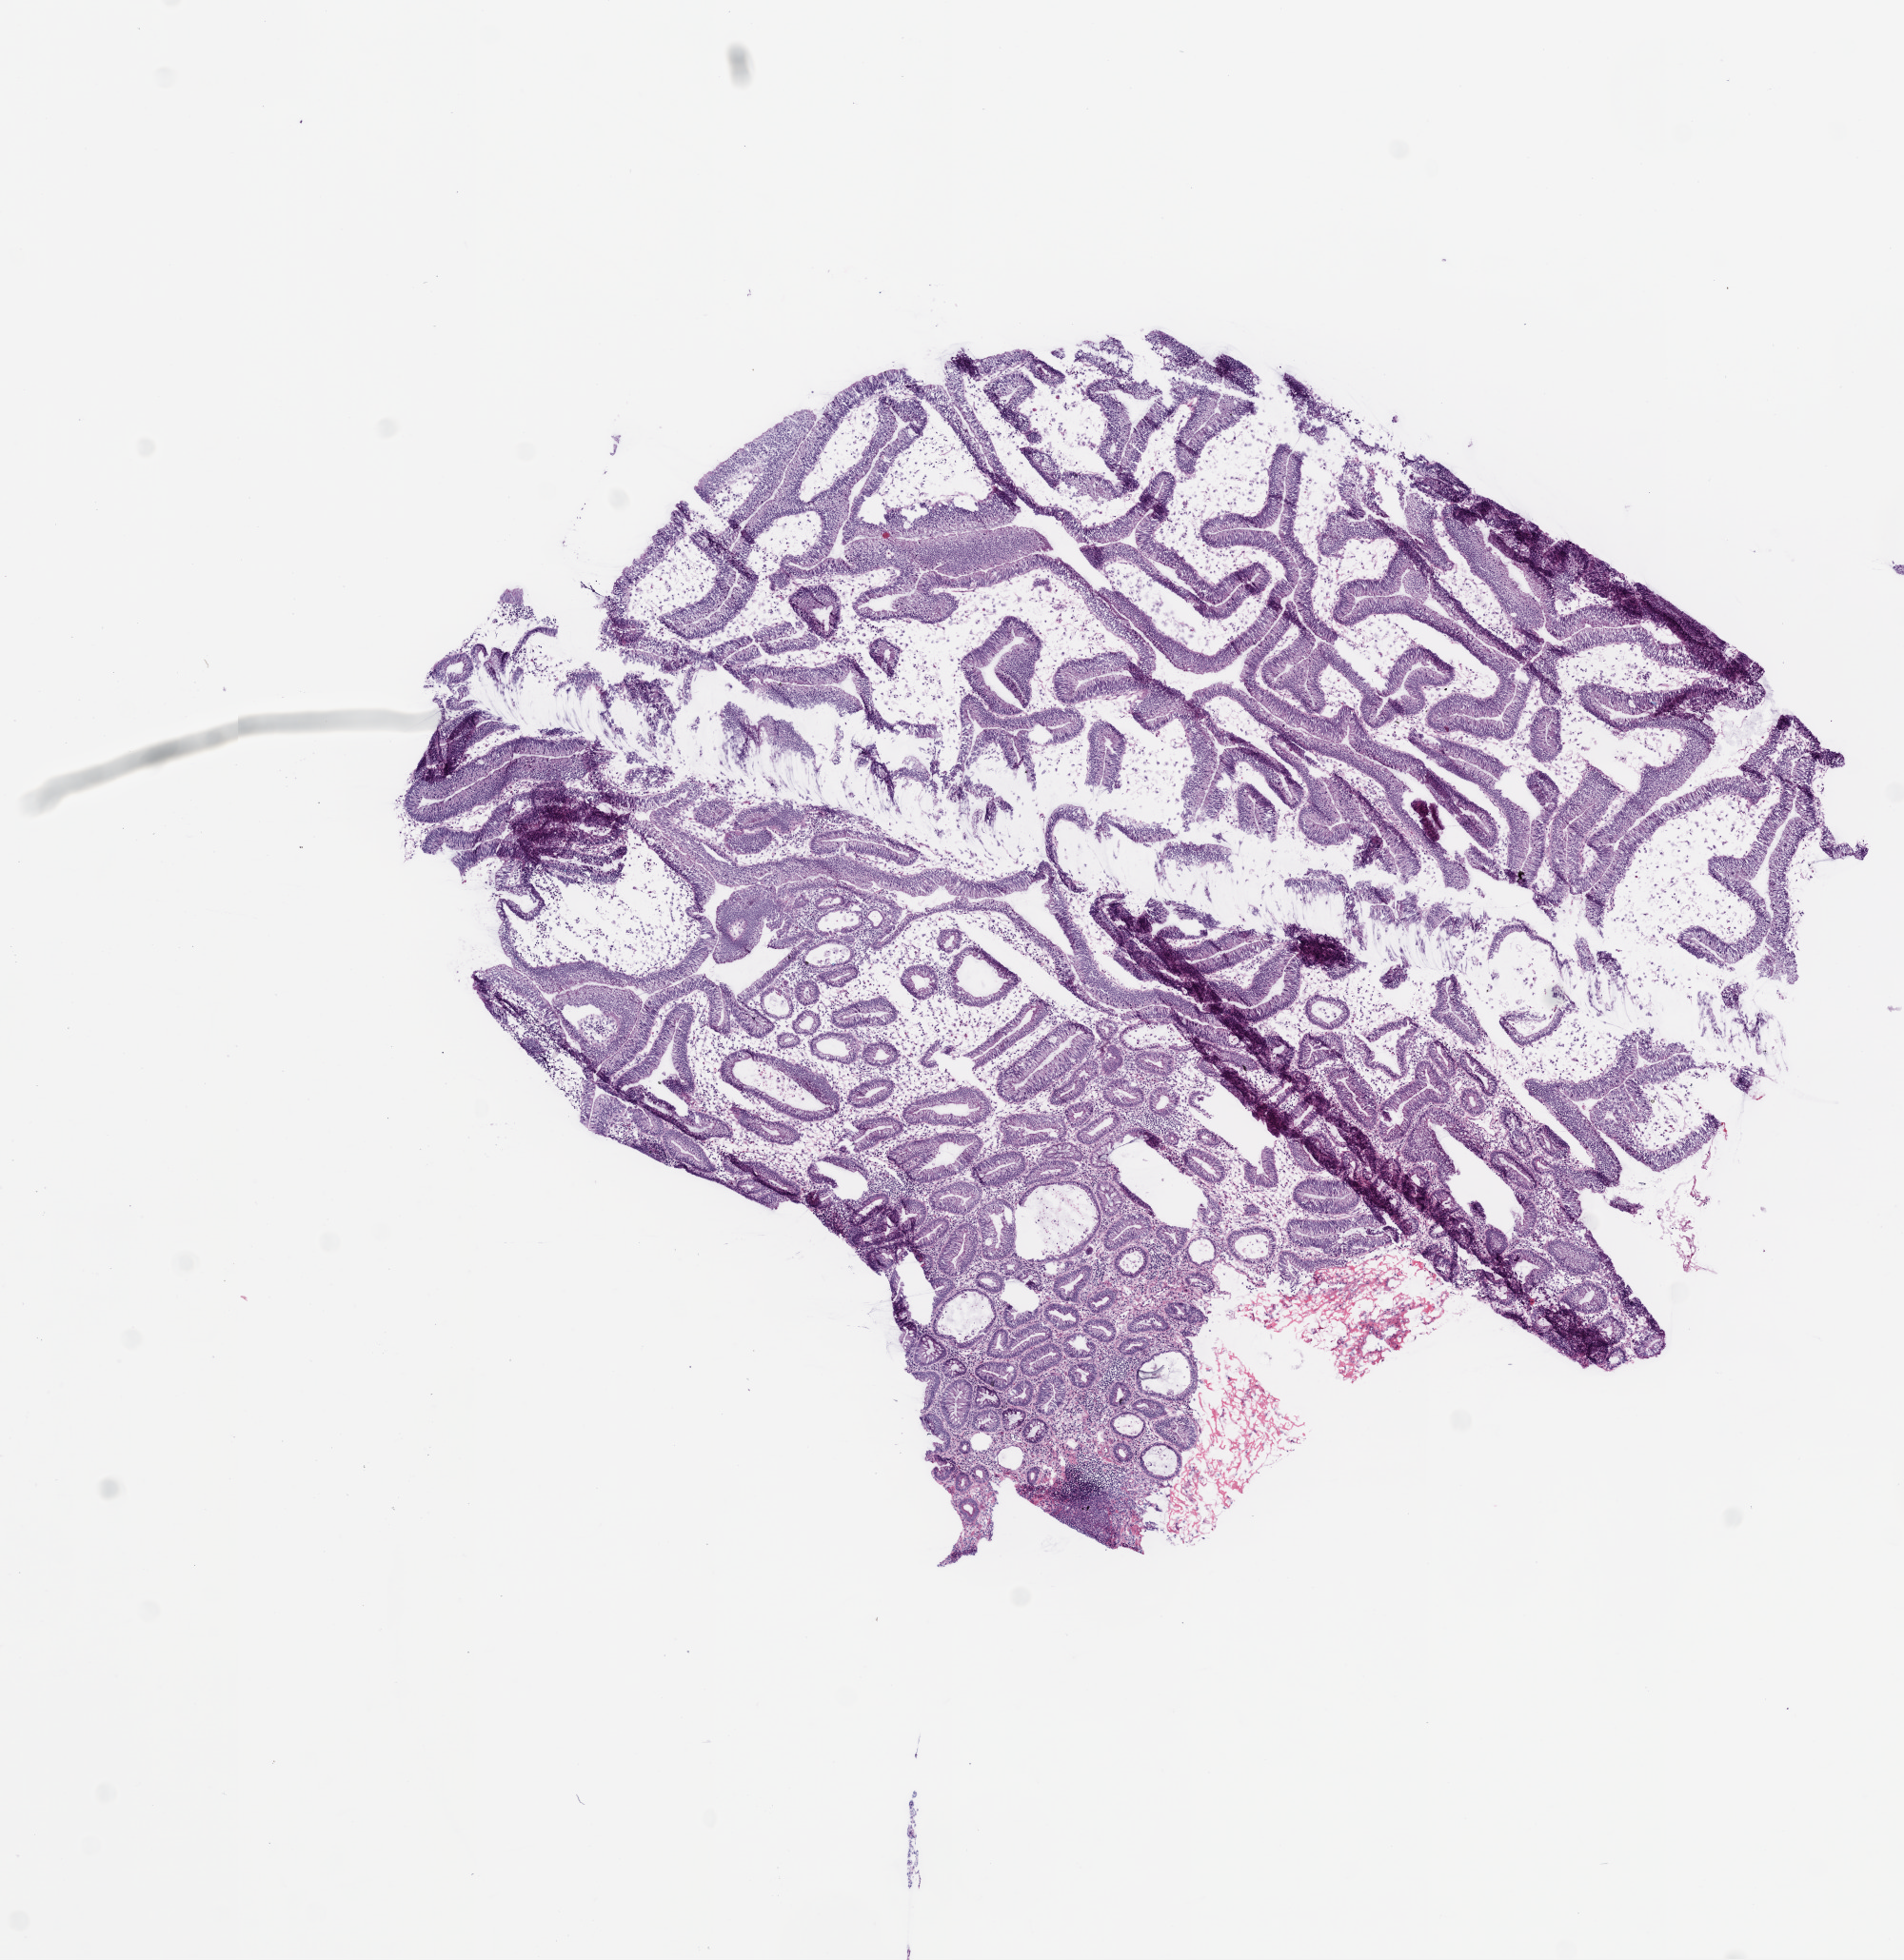
H&E whole-slide image — low-resolution overview of the scanned area, about 8.0 x 8.3 mm. Frozen section from the top of the tissue portion. Rectum, primary tumour sample. Patient: female, age at initial diagnosis 78 years. Composition of this section per pathologist review: tumour cells 85%, tumour nuclei 75%, normal cells 0%, stromal cells 15%, necrosis 0%.
- lymph nodes positive (case pathology): 0 of 12 examined
- AJCC pathologic stage: I (5th edition)
- pathologic diagnosis: Adenocarcinoma, NOS